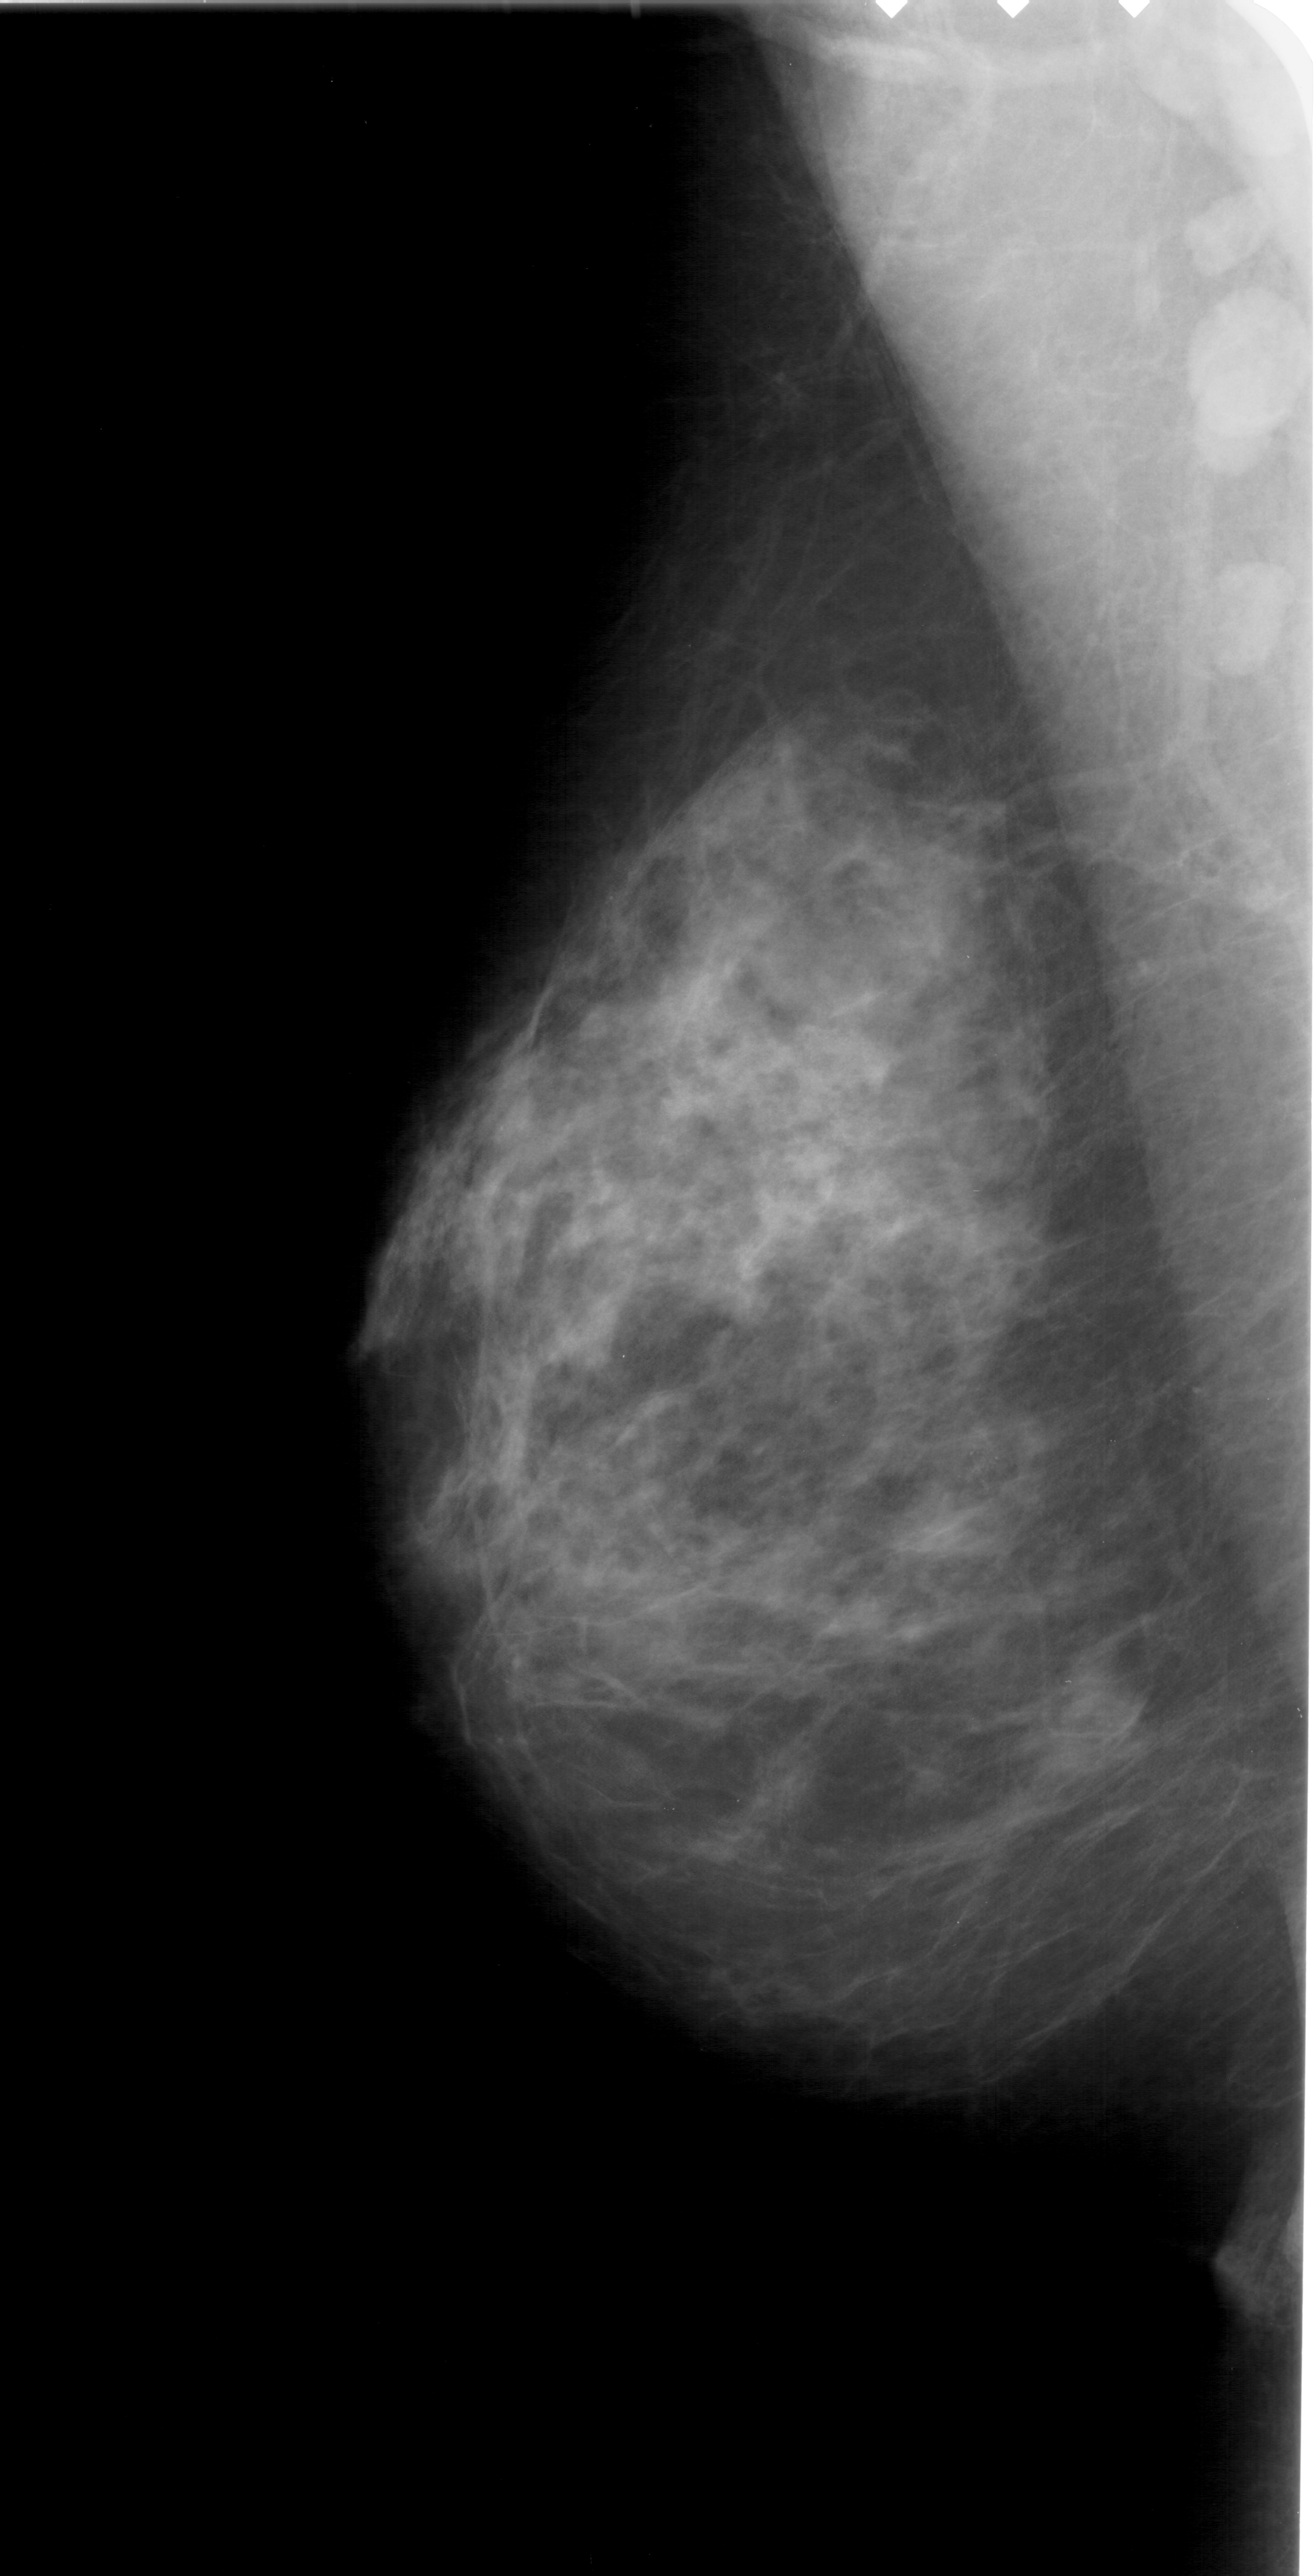
Scanned film-screen mammogram, left breast, MLO view, BI-RADS breast density category 3 (scale 1–4).
Calcifications, morphology pleomorphic, distribution clustered; BI-RADS assessment category 4; pathology (as recorded): benign.